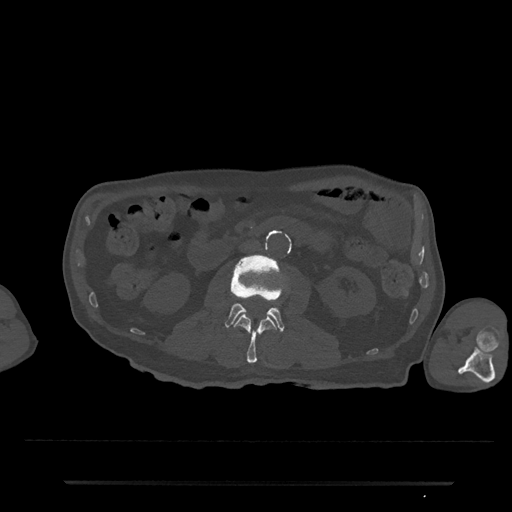
CT including the spine, one axial slice. Slice 23 of 797 in the series (ordered by position). Reconstruction kernel Br40s/3. 120 kVp. Bone window (W 1800 / L 400 HU). 512 × 512 image matrix. Male patient, age 74 years. From the clinical record (not read from this slice): primary cancer: prostate.
Annotated regions visible in this slice (semi-automatic segmentation, software-assisted and operator-edited):
- L2 vertebra: bounding box (x1, y1, x2, y2) in pixels: (234, 315, 276, 364)
- L3 vertebra: (225, 255, 285, 332)